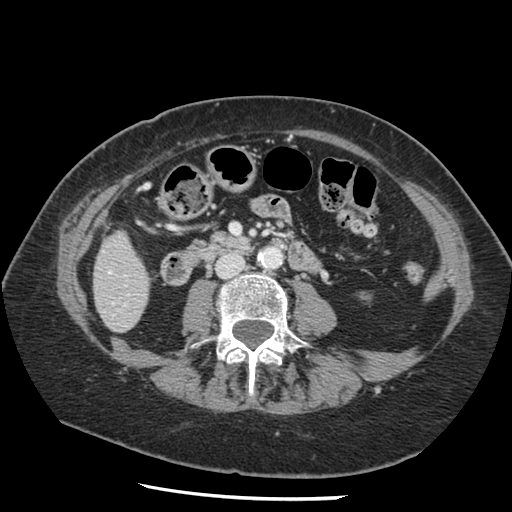
Contrast-enhanced abdominal CT, one axial slice; reconstruction kernel STANDARD; 120 kVp; intravenous contrast given; soft-tissue window (W 400 / L 40 HU); 2.5 mm slice thickness; 512 × 512 image matrix, field of view 330 × 330 mm. Female patient, age 85 years. Case-level facts recorded for this patient, not image findings: diagnosis: colorectal cancer liver metastases, imaged before liver resection; multiple liver metastases: no.
Structures marked on this image (manually delineated by an expert):
- liver: box from (x=94, y=233) to (x=150, y=332) px
- planned liver remnant (the part of the liver to remain after resection): (x=94, y=233)–(x=150, y=332)